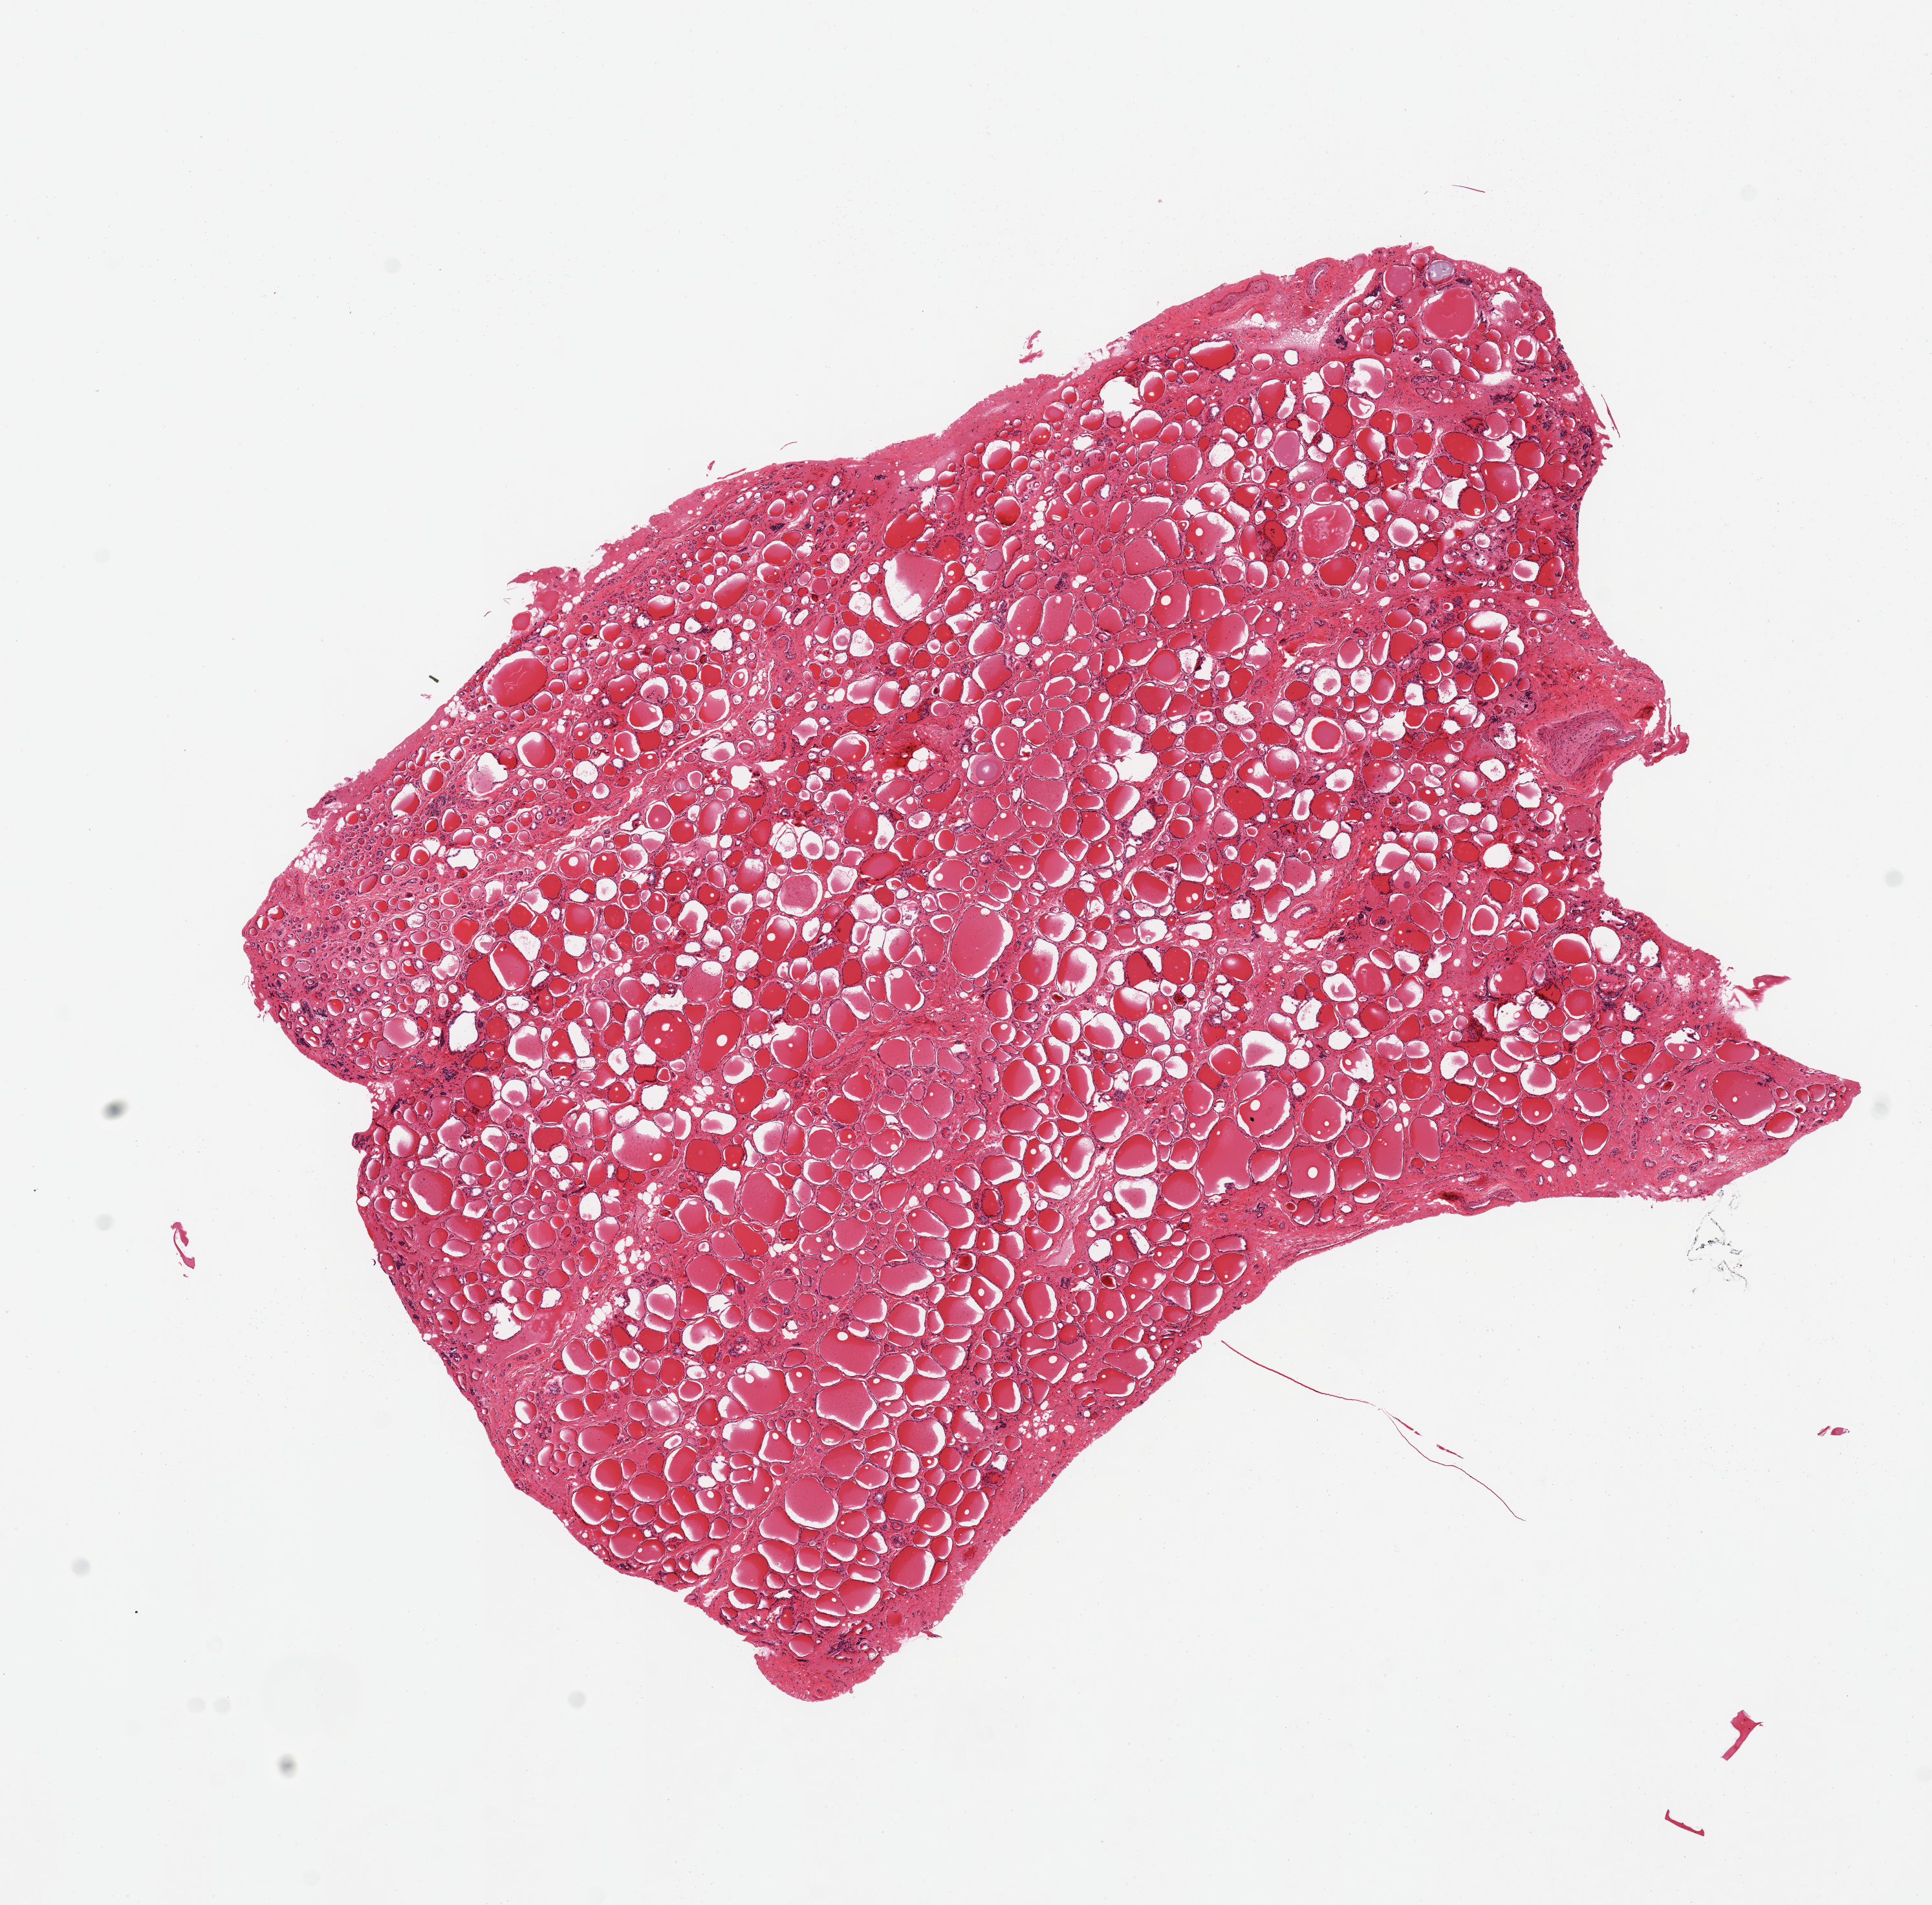
Hematoxylin and eosin (H&E) whole-slide image, brightfield — whole scanned area (about 11.8 x 11.7 mm, slide scanned at 20x) shown as a low-resolution overview. PAXgene-fixed paraffin-embedded (PFPE) section. Sampled site (target tissue): thyroid. Tissue donor sample. Female donor.
Reviewer comment on this tissue sample: 1 piece, no significant abnormalities.